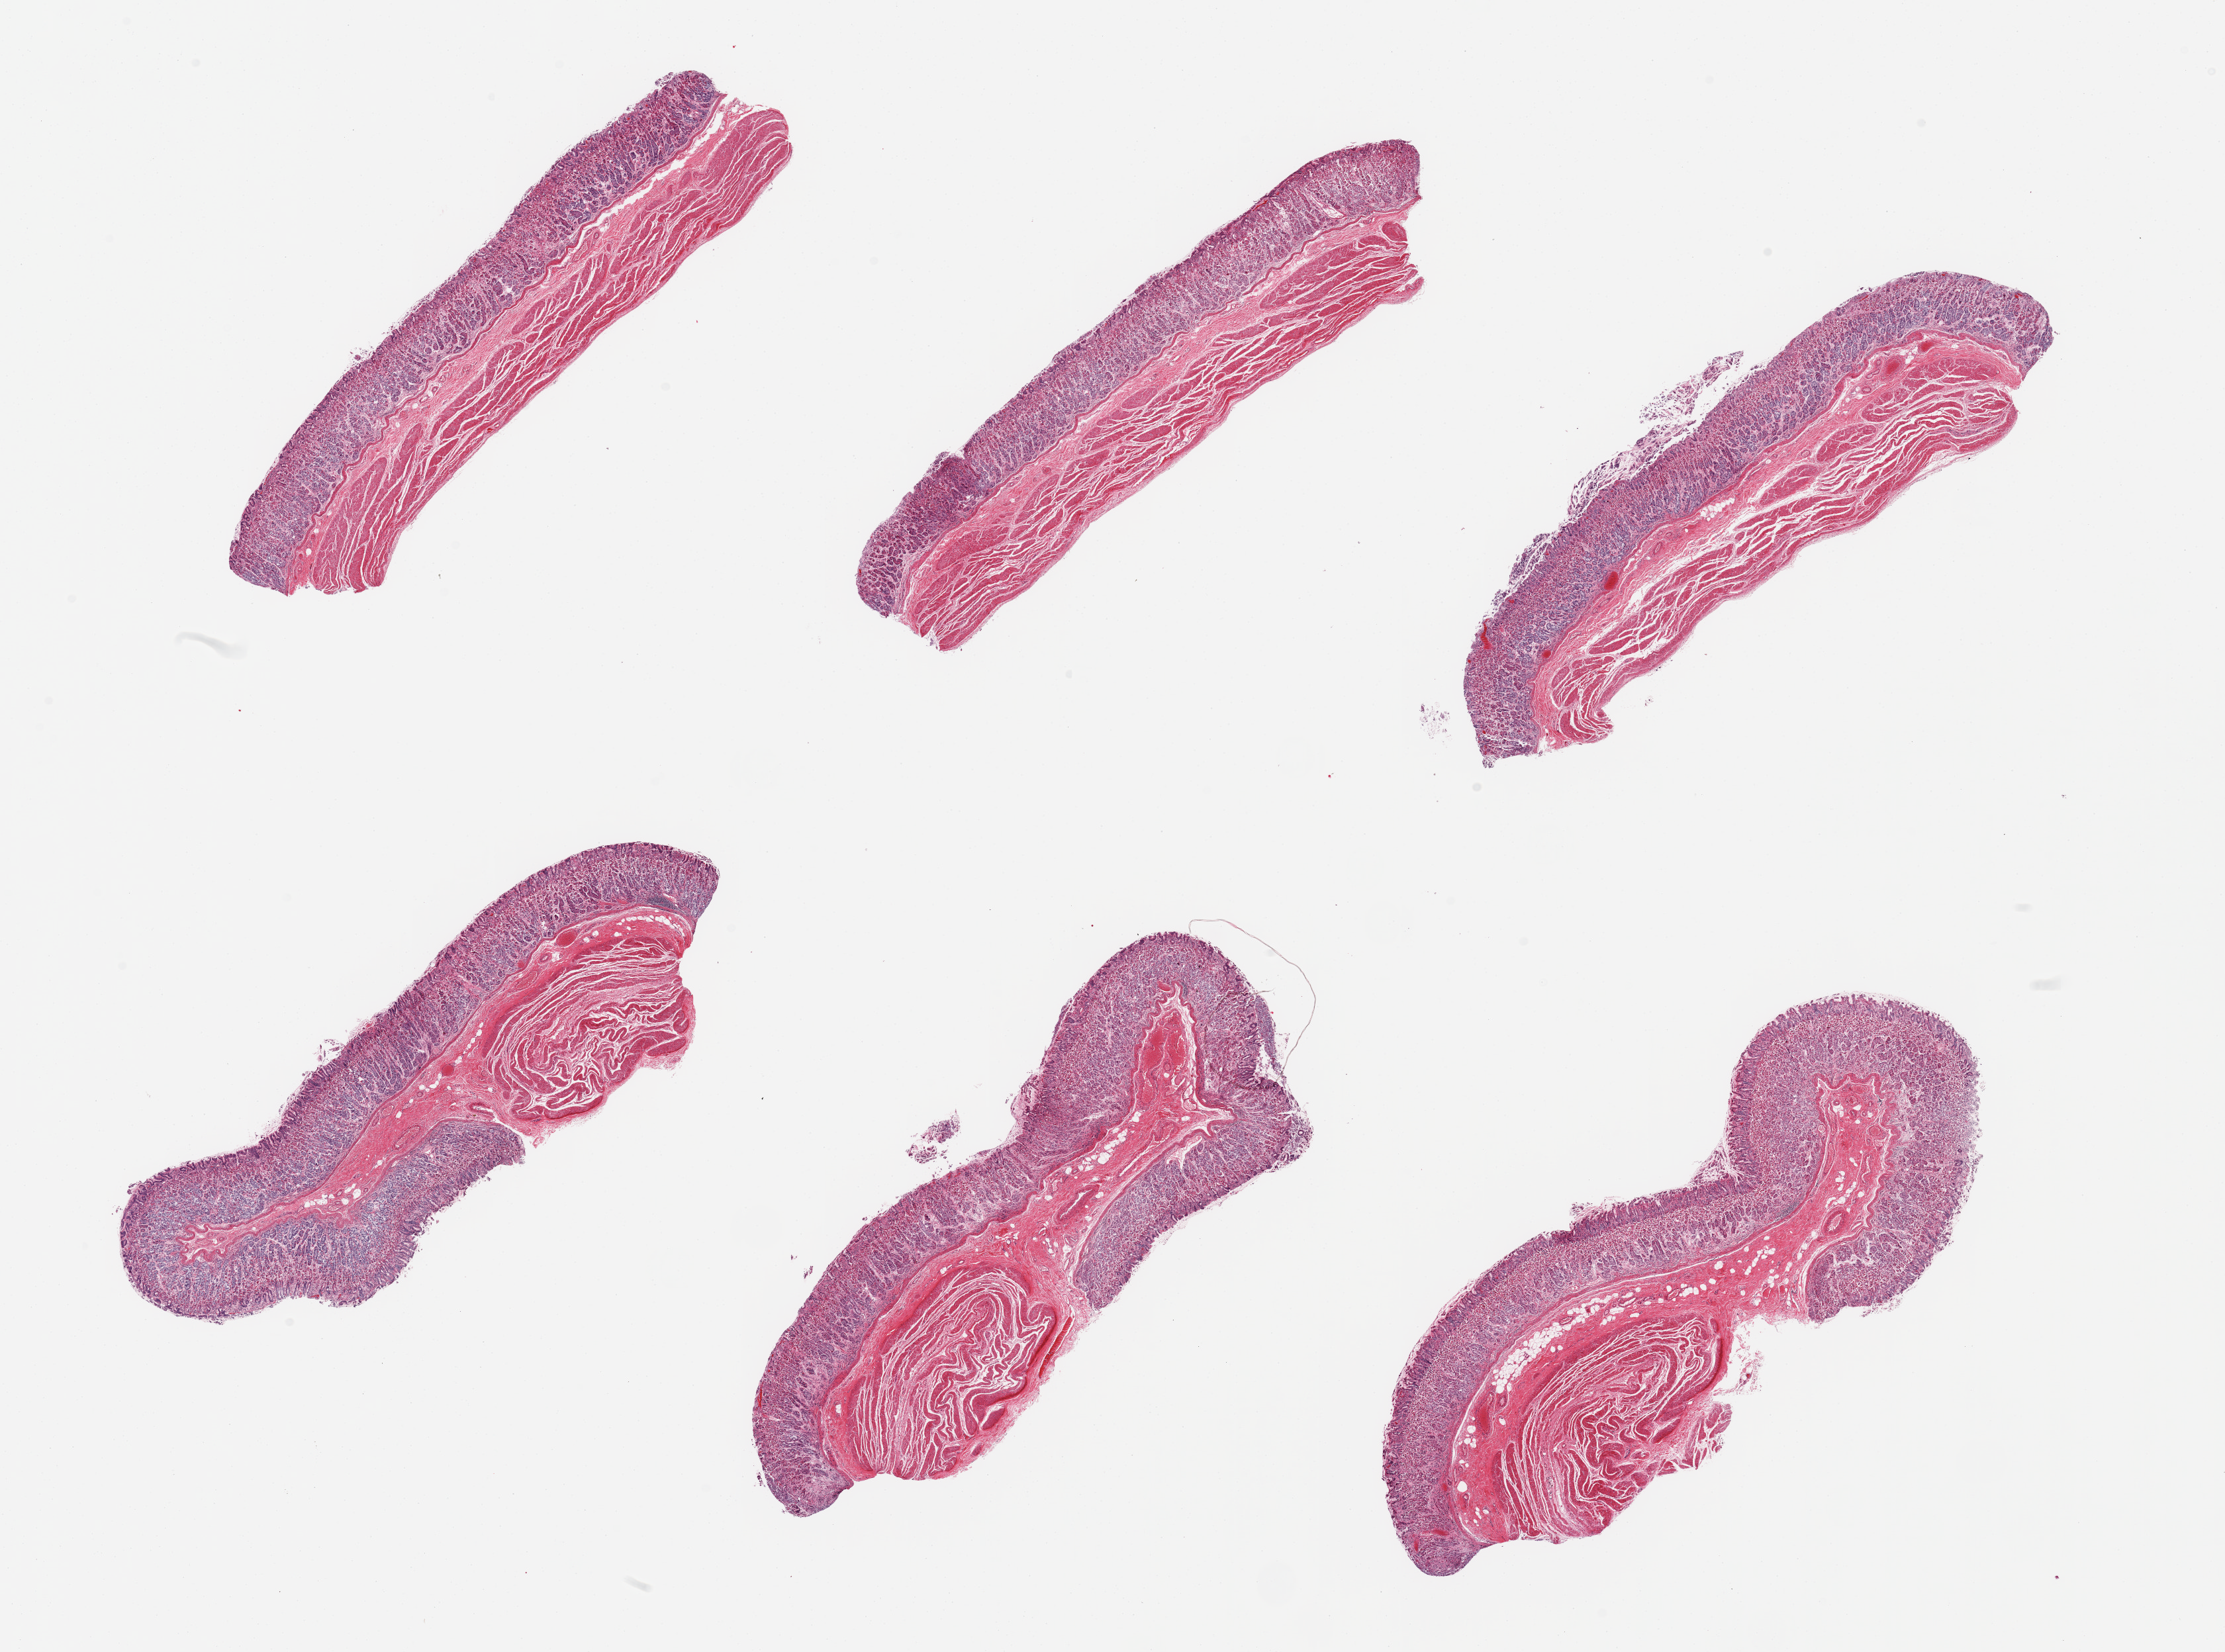
H&E whole-slide image, brightfield, whole scanned area (about 26.6 x 19.7 mm) shown as a low-resolution overview; PAXgene-fixed, paraffin-embedded tissue; target tissue: stomach; donor tissue sample. Male donor.
- review note (as recorded): 6 pieces, mucosa is ~50% thickness, ~moderately autolyzed